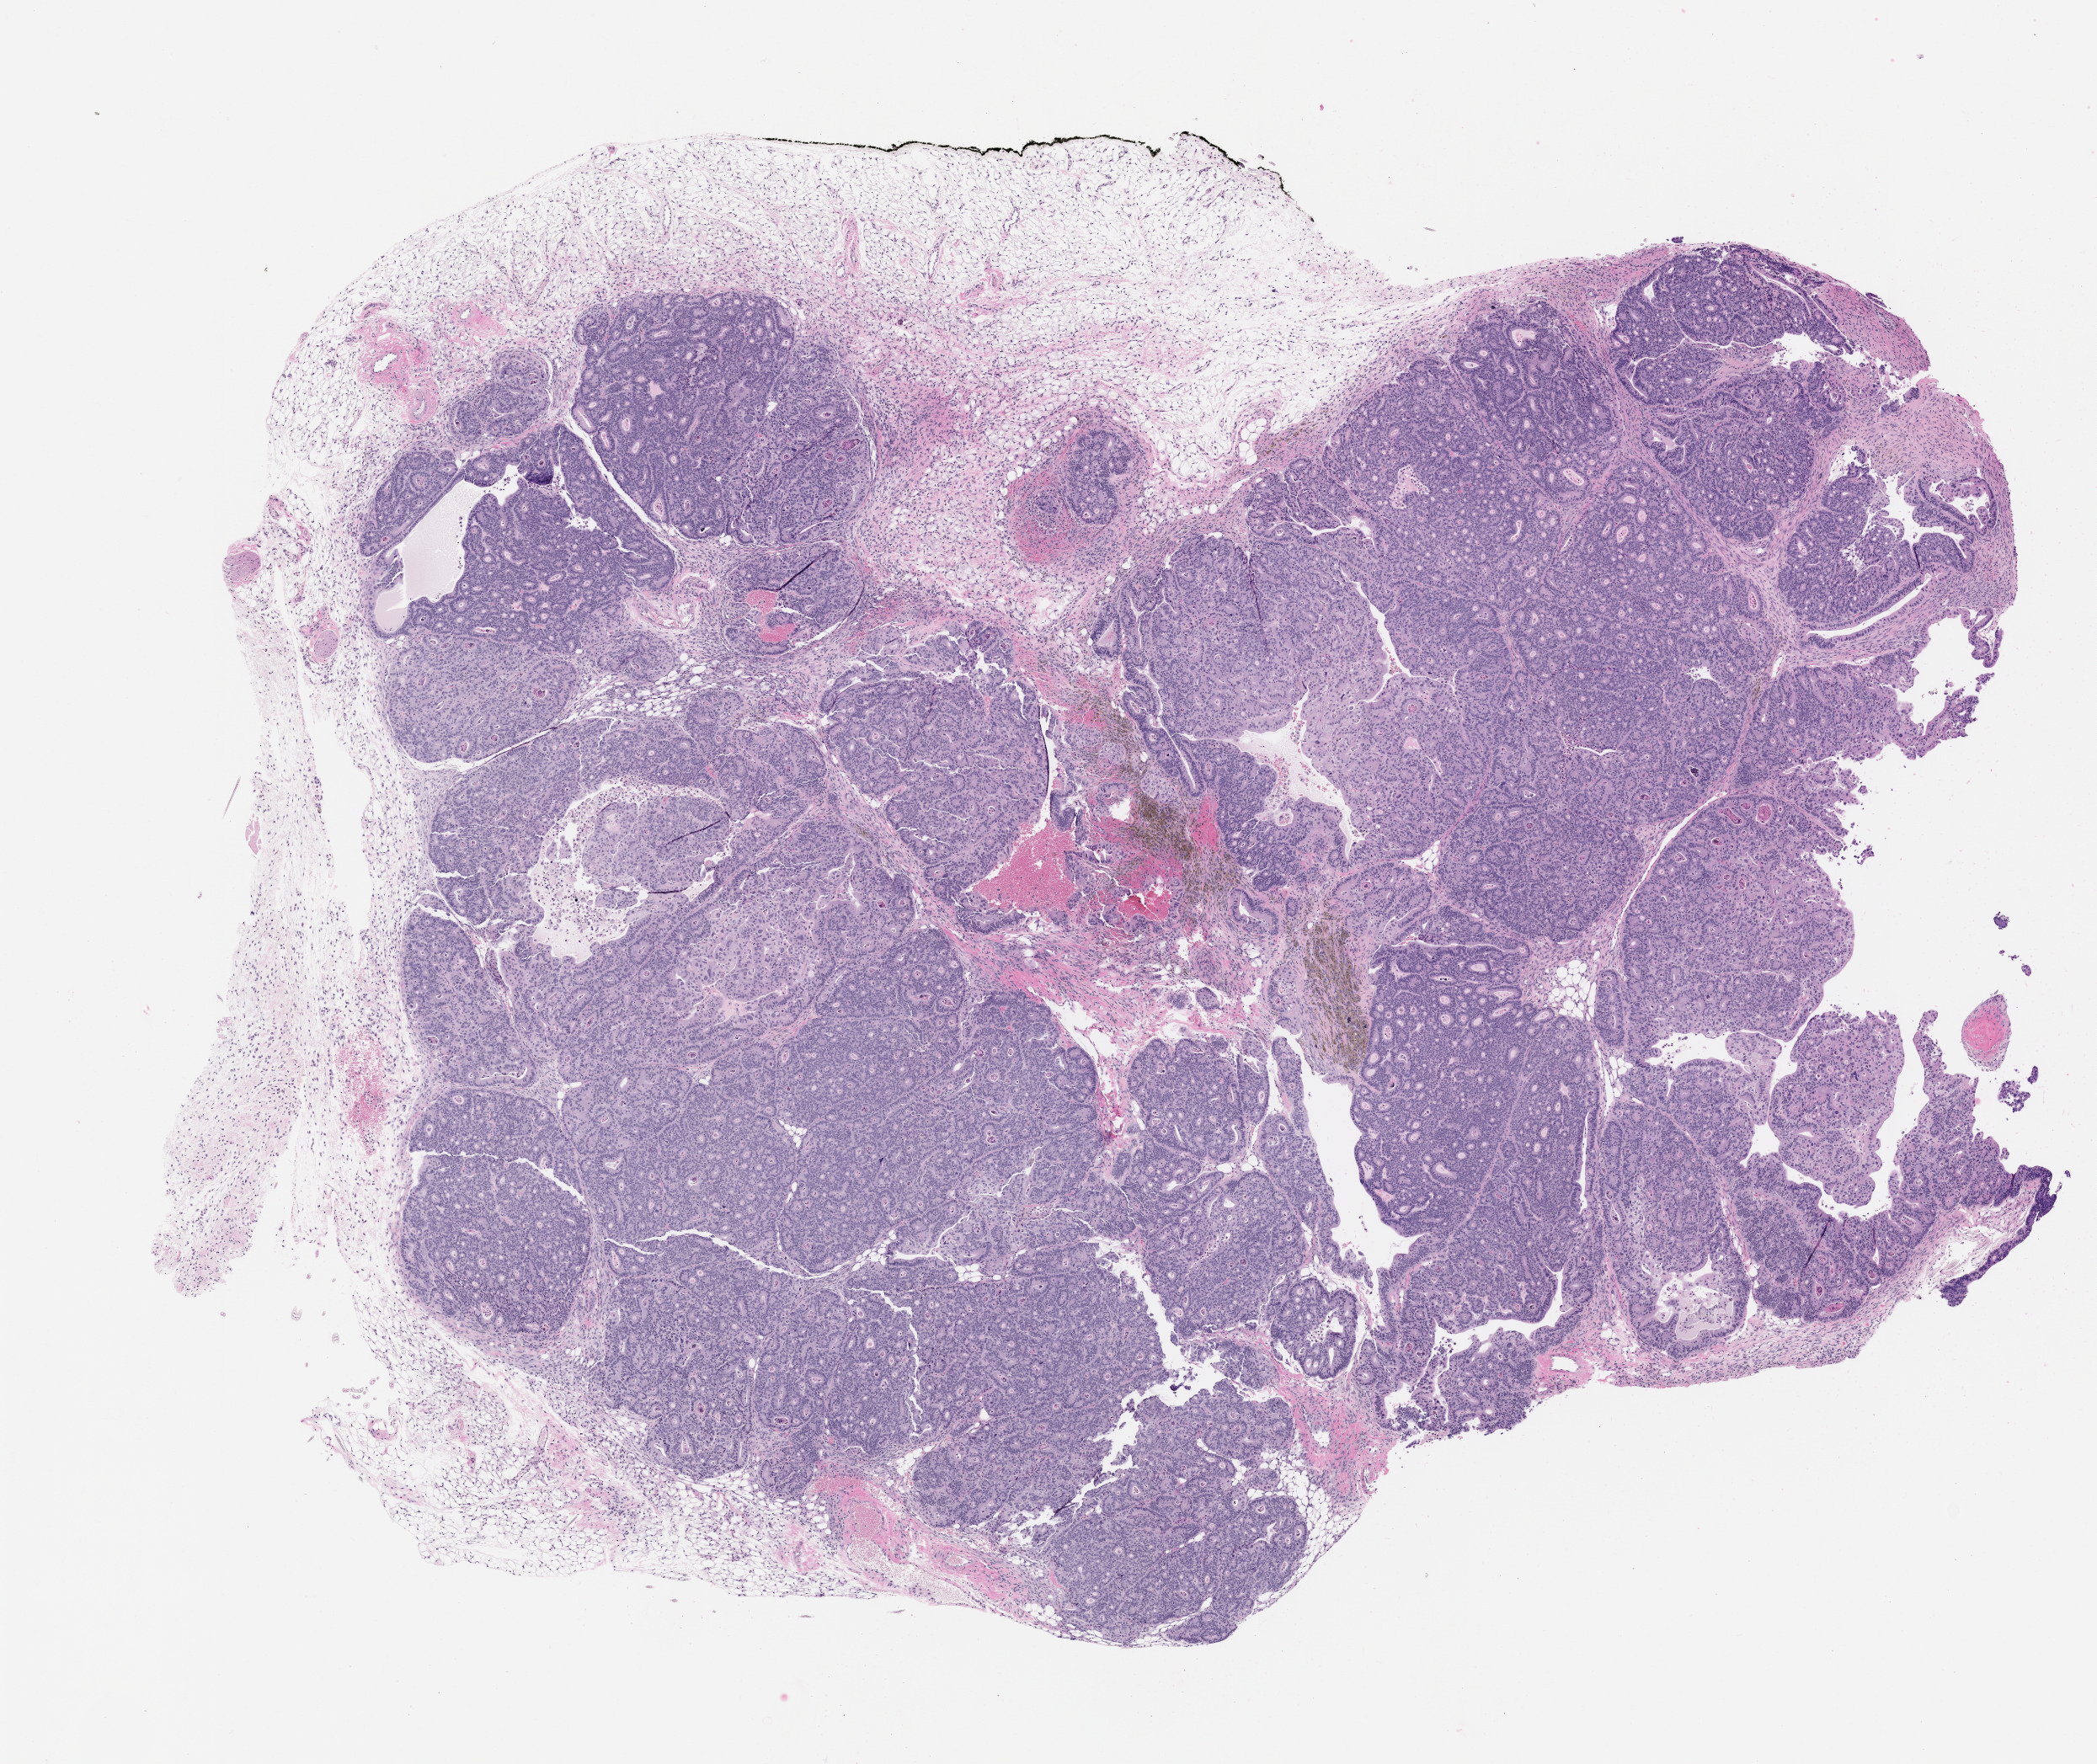
Whole-slide image, H&E: patient-derived xenograft (human tumor grown in a mouse), passage 0, whole scanned area (about 10.0 x 8.4 mm) shown as a low-resolution overview; FFPE section; tumor site category: colon.
Originating patient diagnosis: Colon Adenocarcinoma.